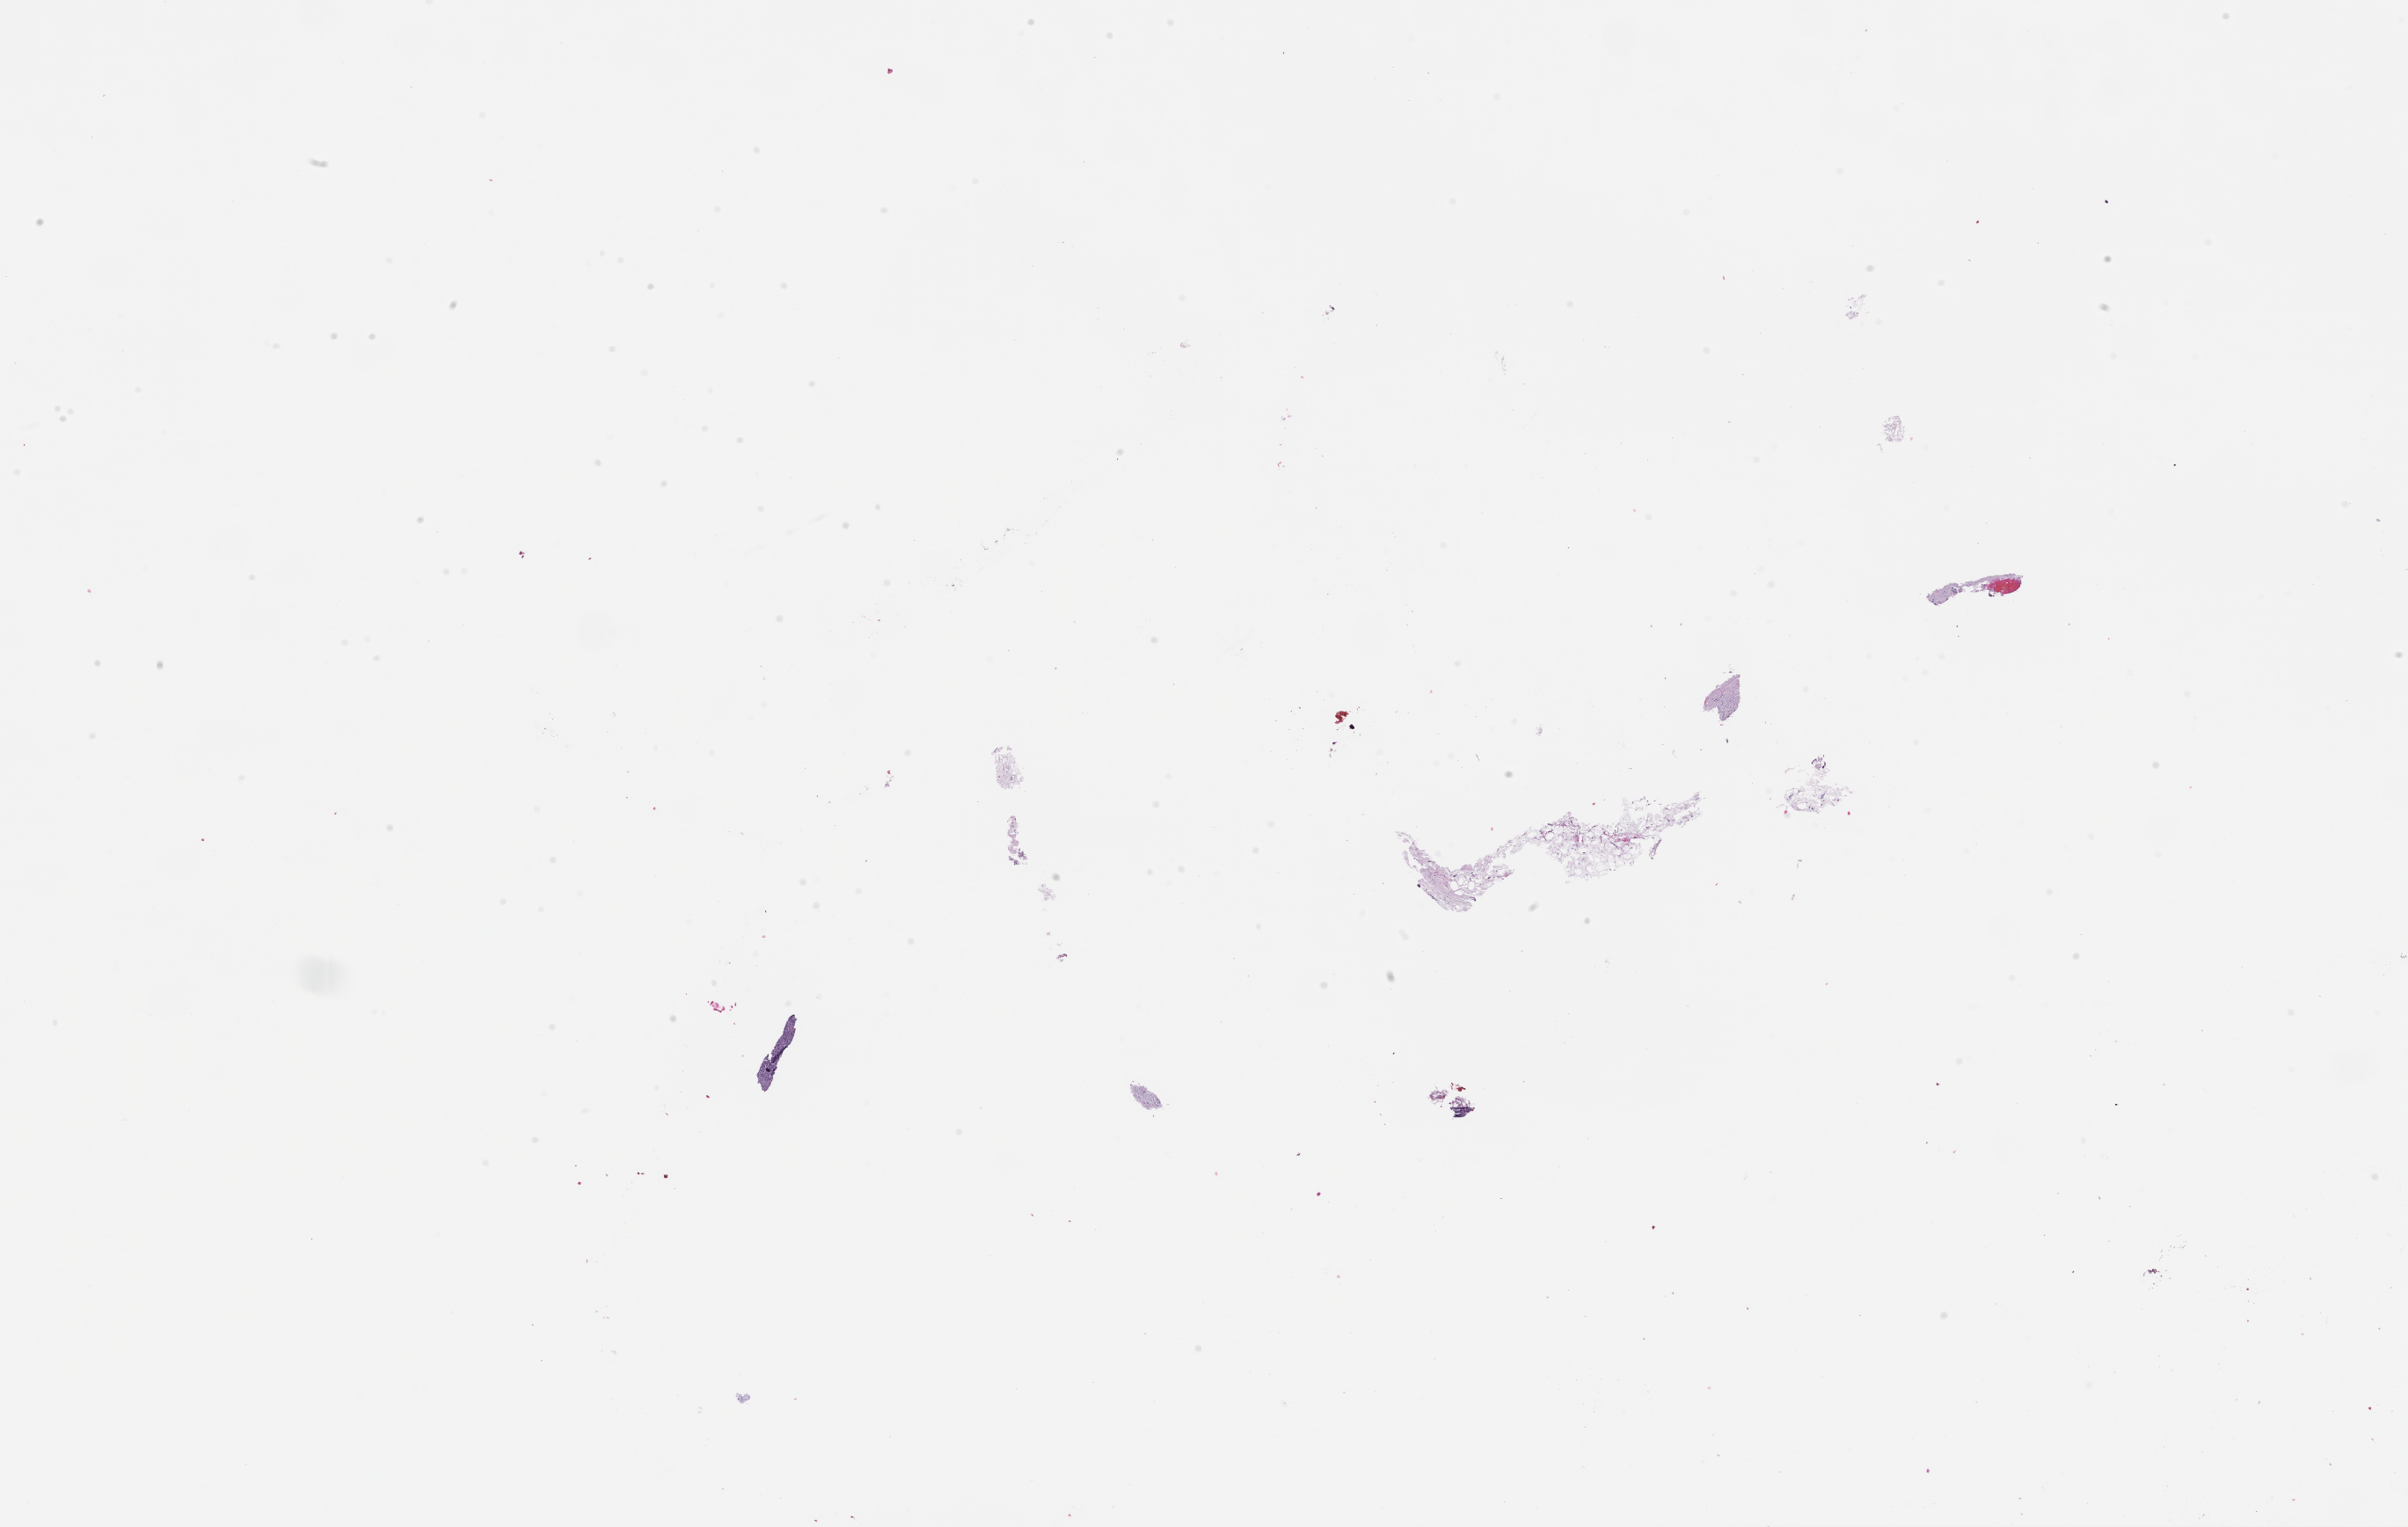
Whole-slide image, haematoxylin and eosin stain, low-resolution overview of the scanned area, about 22.1 x 14.0 mm. Formalin-fixed paraffin-embedded section. Patient: male.
This section: metastatic tumor tissue. Primary diagnosis of the patient: Esophageal Carcinoma.